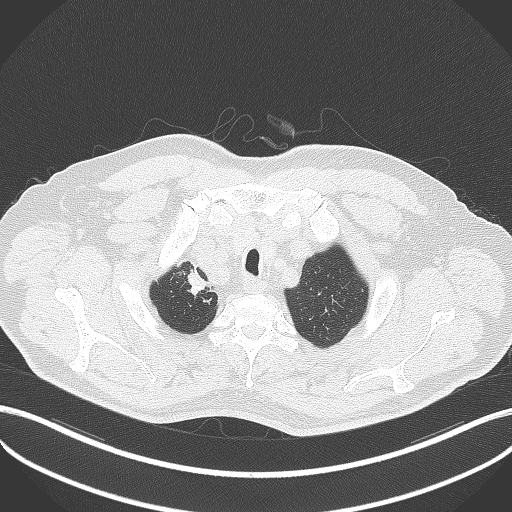
Chest CT, one axial slice; slice 346 of 411 in the series (ordered by position); reconstruction kernel B70f; 120 kVp; lung window (W 1500 / L -600 HU); 1 mm slice thickness; 512 × 512 image matrix, field of view 400 × 400 mm. Male patient, age 60 years. Case-level facts recorded for this patient, not image findings: clinical TNM (as recorded): T1b N1 M0.
Structures marked on this image (rectangle marked by the reading radiologist):
- lung tumour (recorded histology: squamous cell carcinoma): bounding box [x1, y1, x2, y2] px = [185, 270, 206, 296]